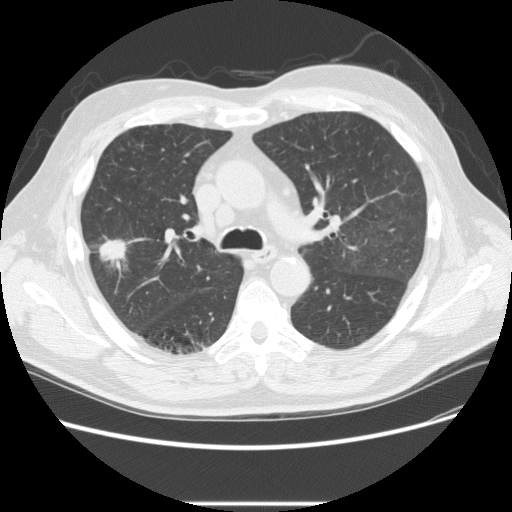
Low-dose screening chest CT, one axial slice. Slice 149 of 233 in the series (ordered by position). Reconstruction kernel STANDARD. 120 kVp. Lung window (W 1500 / L -600 HU). 2.5 mm slice thickness. 512 × 512 image matrix, field of view 380 × 380 mm.
Structures marked on this image (expert manual segmentation):
- lesion 2 (tumor, upper lobe of right lung): bounding box [x1, y1, x2, y2] px = [99, 239, 127, 262]